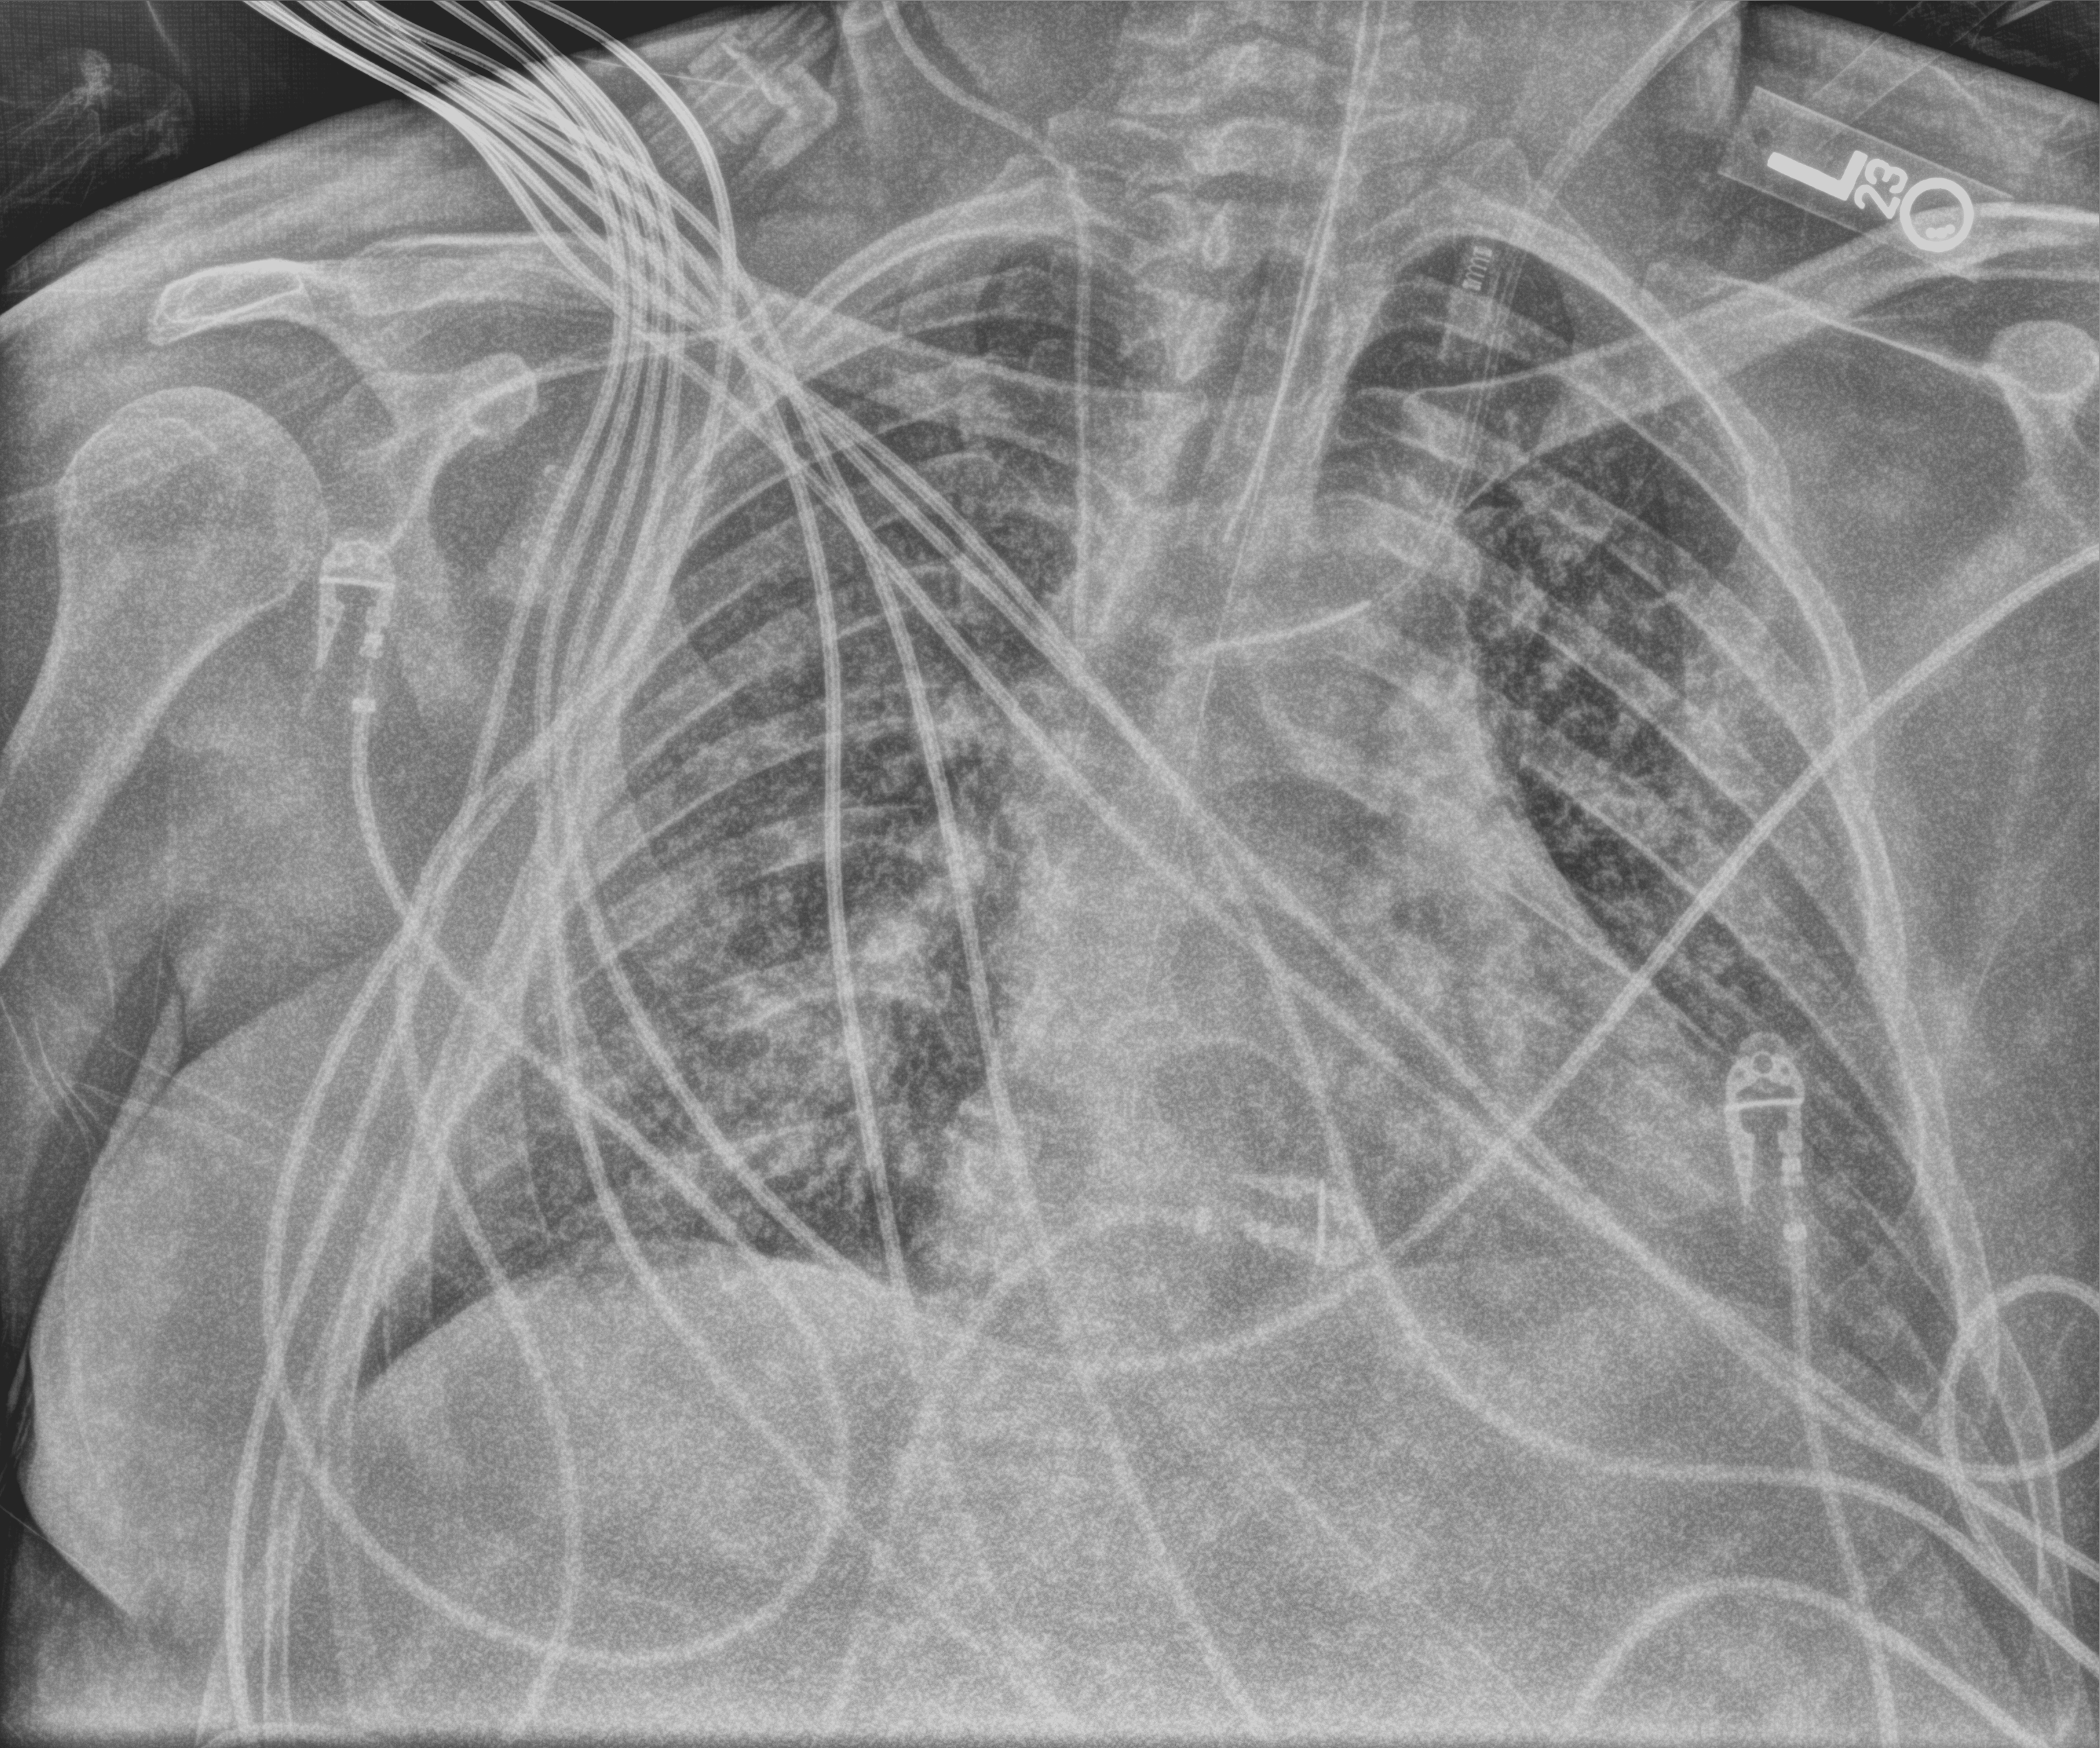
Chest X-ray (portable); anteroposterior (AP) projection. Patient hospitalised with COVID-19; male, aged 18–59 years.
Hospital-stay facts (about this admission, not read from this image; timing relative to this image not recorded): other chronic lung disease (admission record): no; admitted to intensive care during this hospital stay: yes; mechanically ventilated during this hospital stay: yes.